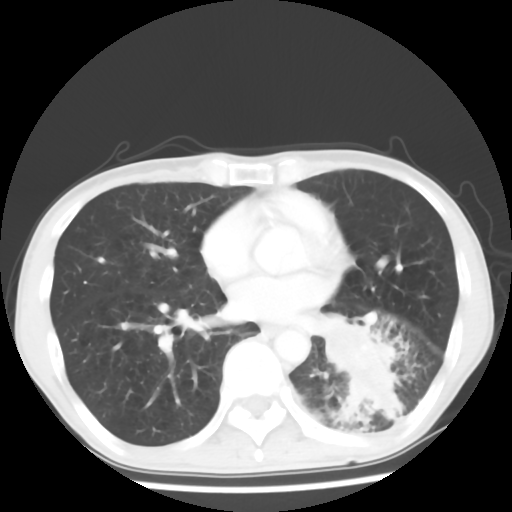
Chest CT, one axial slice. Position 27 of 64 along the scan axis. Reconstruction kernel STANDARD. 120 kVp. Lung window (W 1500 / L -600 HU). 512 × 512 image matrix, field of view 313 × 313 mm. Patient: male, 68 years. Case-level facts recorded for this patient, not image findings: clinical TNM (as recorded): T4 N0 M0.
Annotated regions visible in this slice (rectangle marked by the reading radiologist):
- lung tumour (recorded histology: squamous cell carcinoma): bounding box <313,305,374,371> (left, top, right, bottom; pixels)